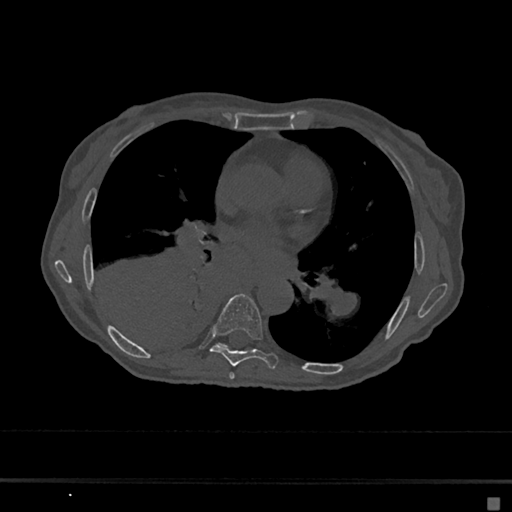
CT including the spine, one axial slice; position 367 of 797 along the scan axis; 120 kVp; bone window (W 1800 / L 400 HU); 512 × 512 image matrix, field of view 360 × 360 mm. Patient: female, 68 years. From the clinical record (not read from this slice): primary cancer: renal.
Structures marked on this image (semi-automatic segmentation, software-assisted and operator-edited):
- T6 vertebra: bounding box [x1, y1, x2, y2] px = [229, 372, 235, 379]
- T7 vertebra: [210, 294, 278, 369]
- T8 vertebra: [221, 345, 226, 347]